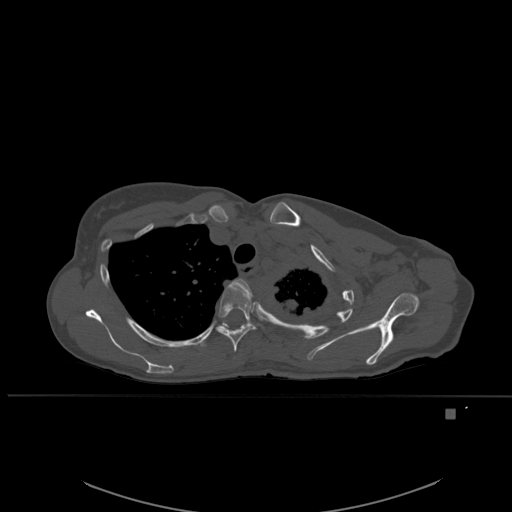
CT including the spine, one axial slice. Slice 412 of 537 in the series (ordered by position). Bone window (W 1800 / L 400 HU). 1.5 mm slice thickness. 512 × 512 image matrix, field of view 440 × 440 mm. Patient: female, 45 years. From the clinical record (not read from this slice): primary cancer: lung.
Structures marked on this image (semi-automatic segmentation, software-assisted and operator-edited):
- T3 vertebra: box from (x=232, y=278) to (x=253, y=296) px
- T4 vertebra: (x=216, y=283)–(x=256, y=353)
- T5 vertebra: (x=198, y=325)–(x=242, y=349)